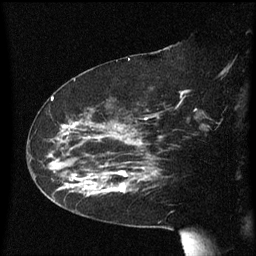
Breast MRI (dynamic contrast-enhanced), one sagittal slice; slice 37 of 60 in the series (ordered by position); dynamic contrast-enhanced series, image 2 of 3 at this slice position (ordered by acquisition); 1.5 T; TE 4.2 ms, TR 8.4 ms; 2.3 mm slice thickness; 256 × 256 image matrix. Patient: female, 63 years. Case-level facts recorded for this patient, not image findings: setting: breast cancer imaged before/during neoadjuvant chemotherapy; receptor status: HER2-positive.
Annotated regions visible in this slice (semi-automatic segmentation, software-assisted and operator-edited):
- analysis volume of interest (the breast-tissue region the enhancement analysis was run in; not a lesion): bounding box <71,144,147,197> (left, top, right, bottom; pixels)
- tumour enhancement mask (voxels above the 70 % enhancement threshold inside the analysis volume of interest): <94,172,147,193>